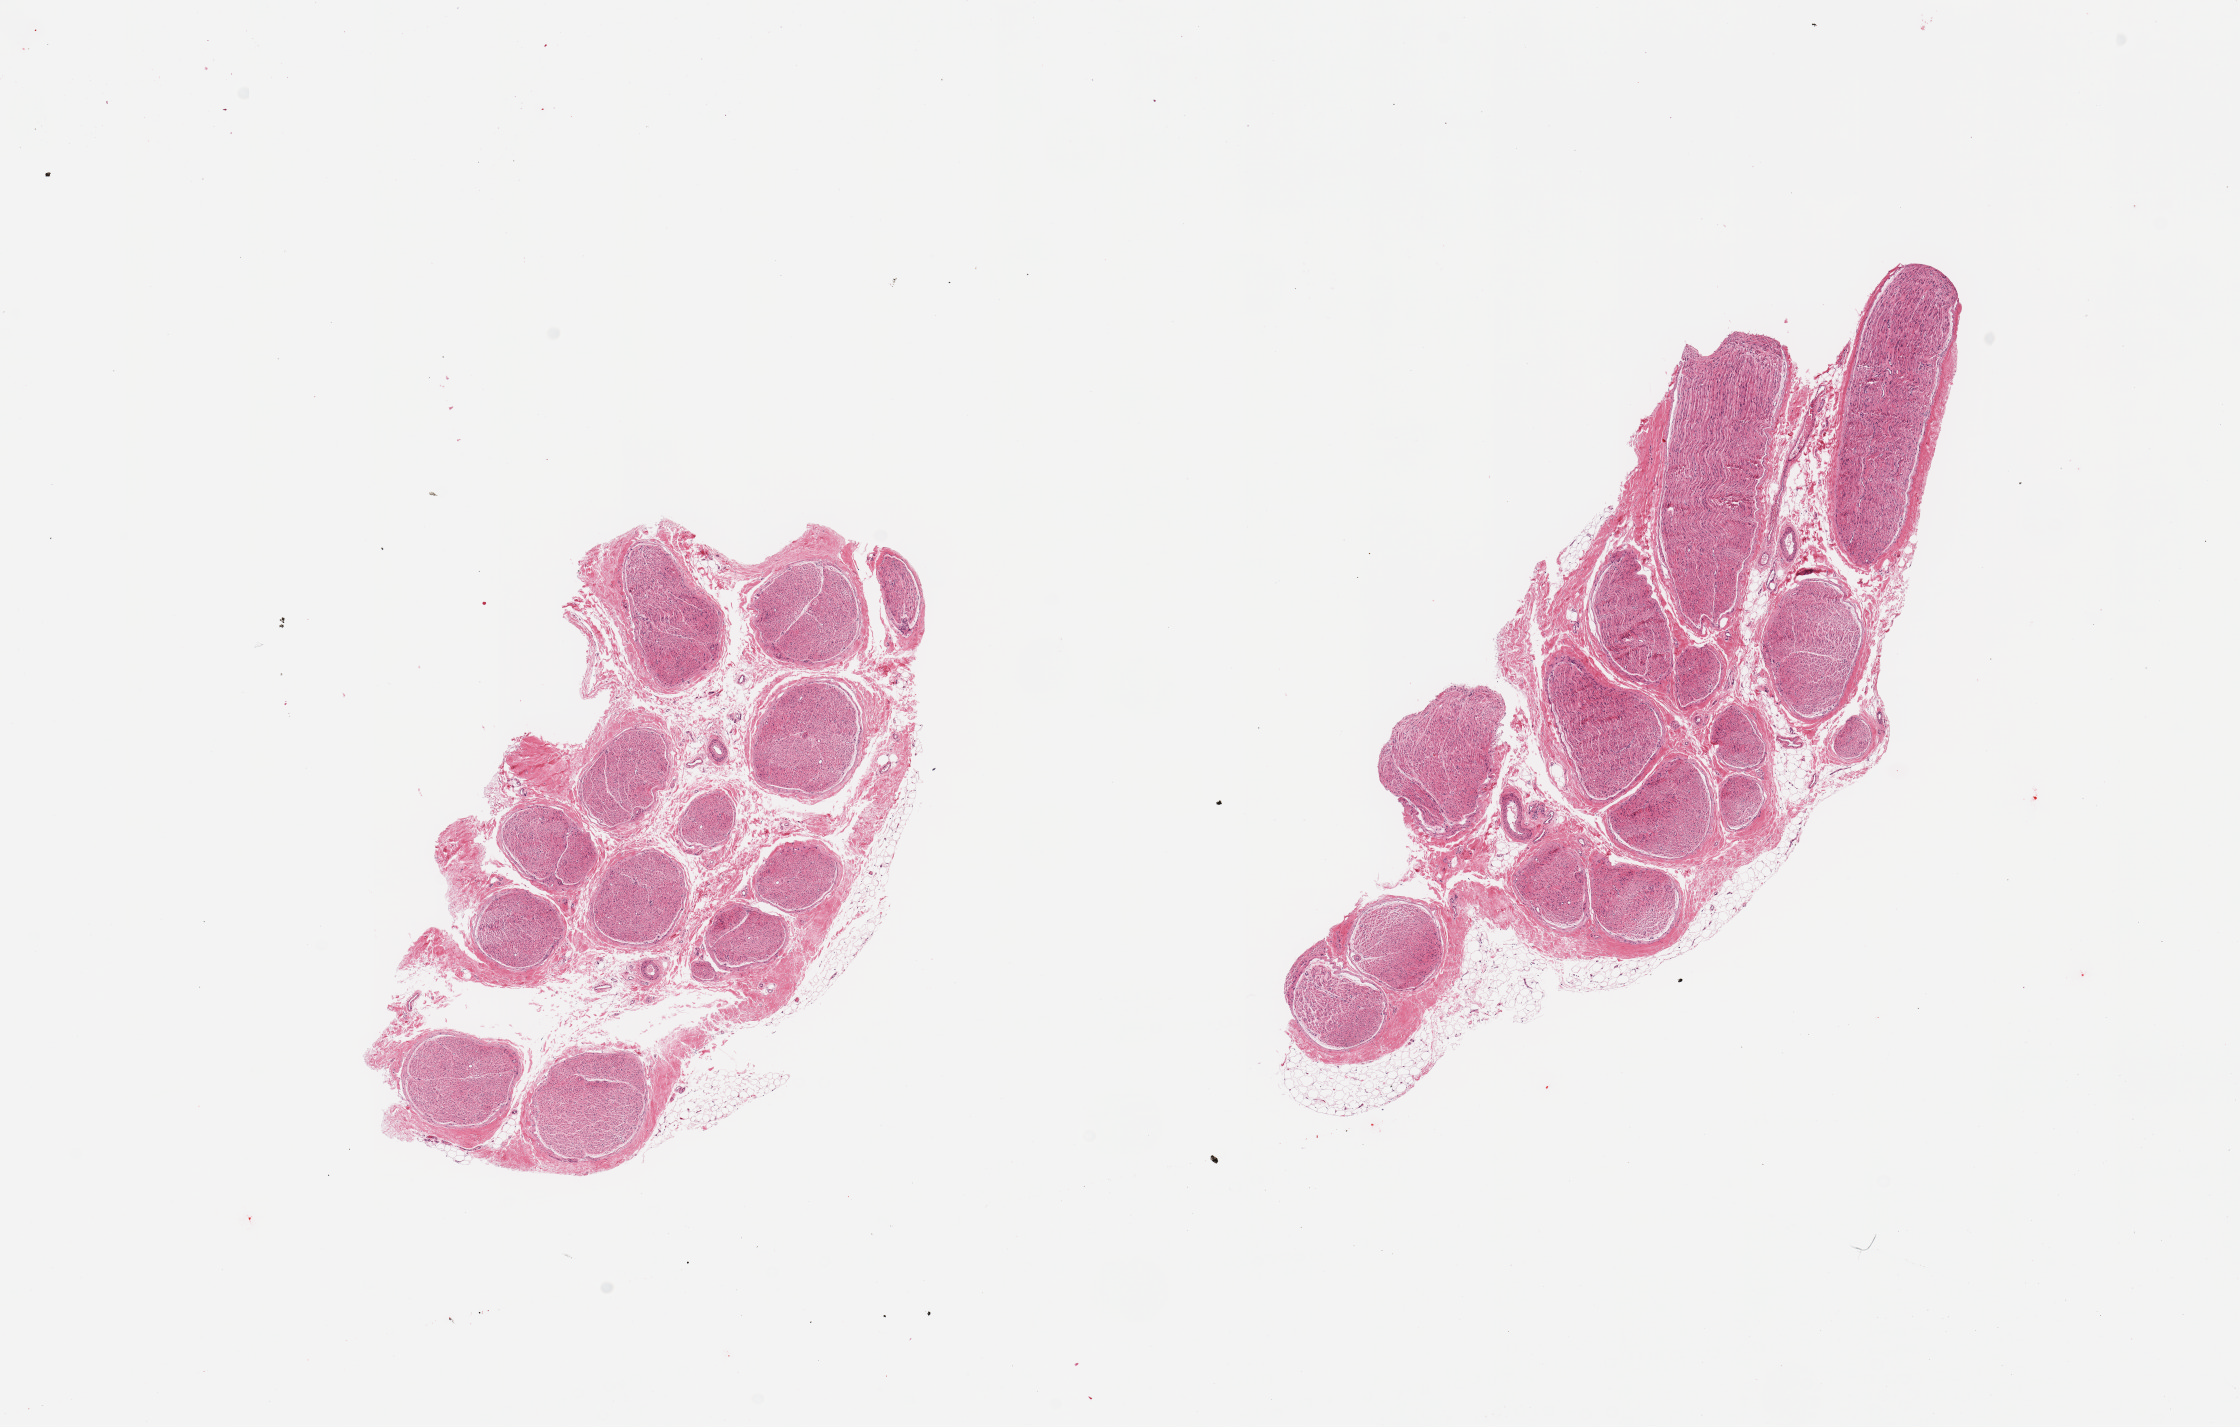
Whole-slide image, hematoxylin and eosin (H&E) stain — low-resolution overview of the scanned area, about 17.7 x 11.3 mm (slide scanned at 20x). PAXgene-fixed paraffin-embedded (PFPE) section. Target tissue: tibial nerve. Tissue donor sample. Donor sex: male.
* reviewer comment on this tissue sample: 2 pieces trace adherent fat, ~0.3mm, focal